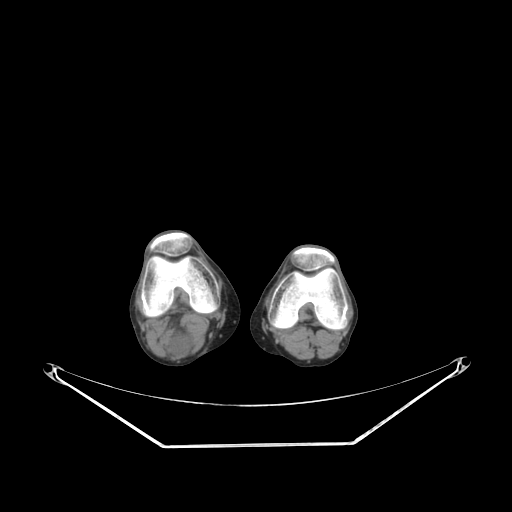
CT of an extremity soft-tissue mass (from a PET/CT study), one axial slice; position 163 of 267 along the scan axis; soft-tissue window (W 400 / L 40 HU); 512 × 512 image matrix. Female patient. From the clinical record (not read from this slice): histological type: liposarcoma; site of the primary tumour: right thigh.
Structures marked on this image (expert contour drawn on MRI and transferred to this co-registered scan by the dataset authors):
- gross tumour volume (mass): bounding box <169,336,190,355> (left, top, right, bottom; pixels)